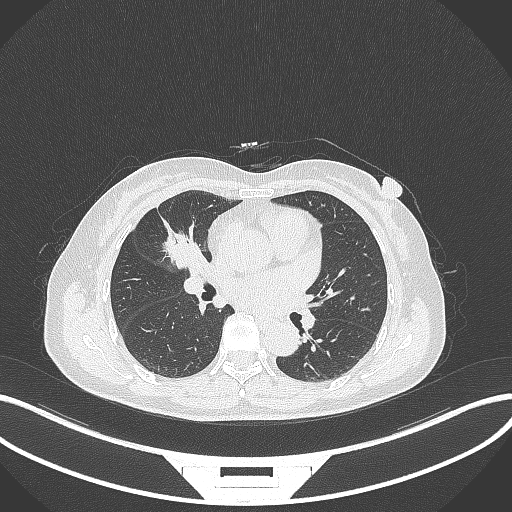
Chest CT, one axial slice. Position 156 of 284 along the scan axis. Reconstruction kernel B70f. 120 kVp. Lung window (W 1500 / L -600 HU). 1 mm slice thickness. 512 × 512 image matrix, field of view 400 × 400 mm. Patient: female, 51 years. Case-level facts recorded for this patient, not image findings: clinical TNM (as recorded): T1c N0 M0; histopathological grade: G2.
Annotated regions visible in this slice (bounding box drawn by a radiologist):
- lung tumour (recorded histology: adenocarcinoma): box from (x=157, y=225) to (x=201, y=268) px